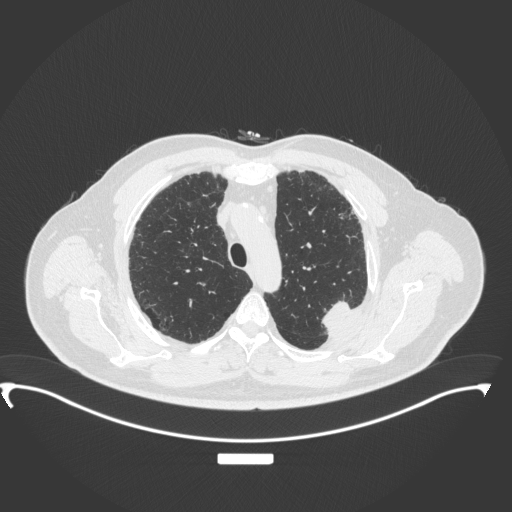
Chest CT, one axial slice; position 278 of 350 along the scan axis; lung window (W 1500 / L -600 HU); 1 mm slice thickness; 512 × 512 image matrix. Male patient, age 64 years. From the clinical record (not read from this slice): clinical TNM (as recorded): T1c N1 M1.
Structures marked on this image (bounding box drawn by a radiologist):
- lung tumour (recorded histology: adenocarcinoma): bounding box [x1, y1, x2, y2] px = [317, 294, 357, 333]